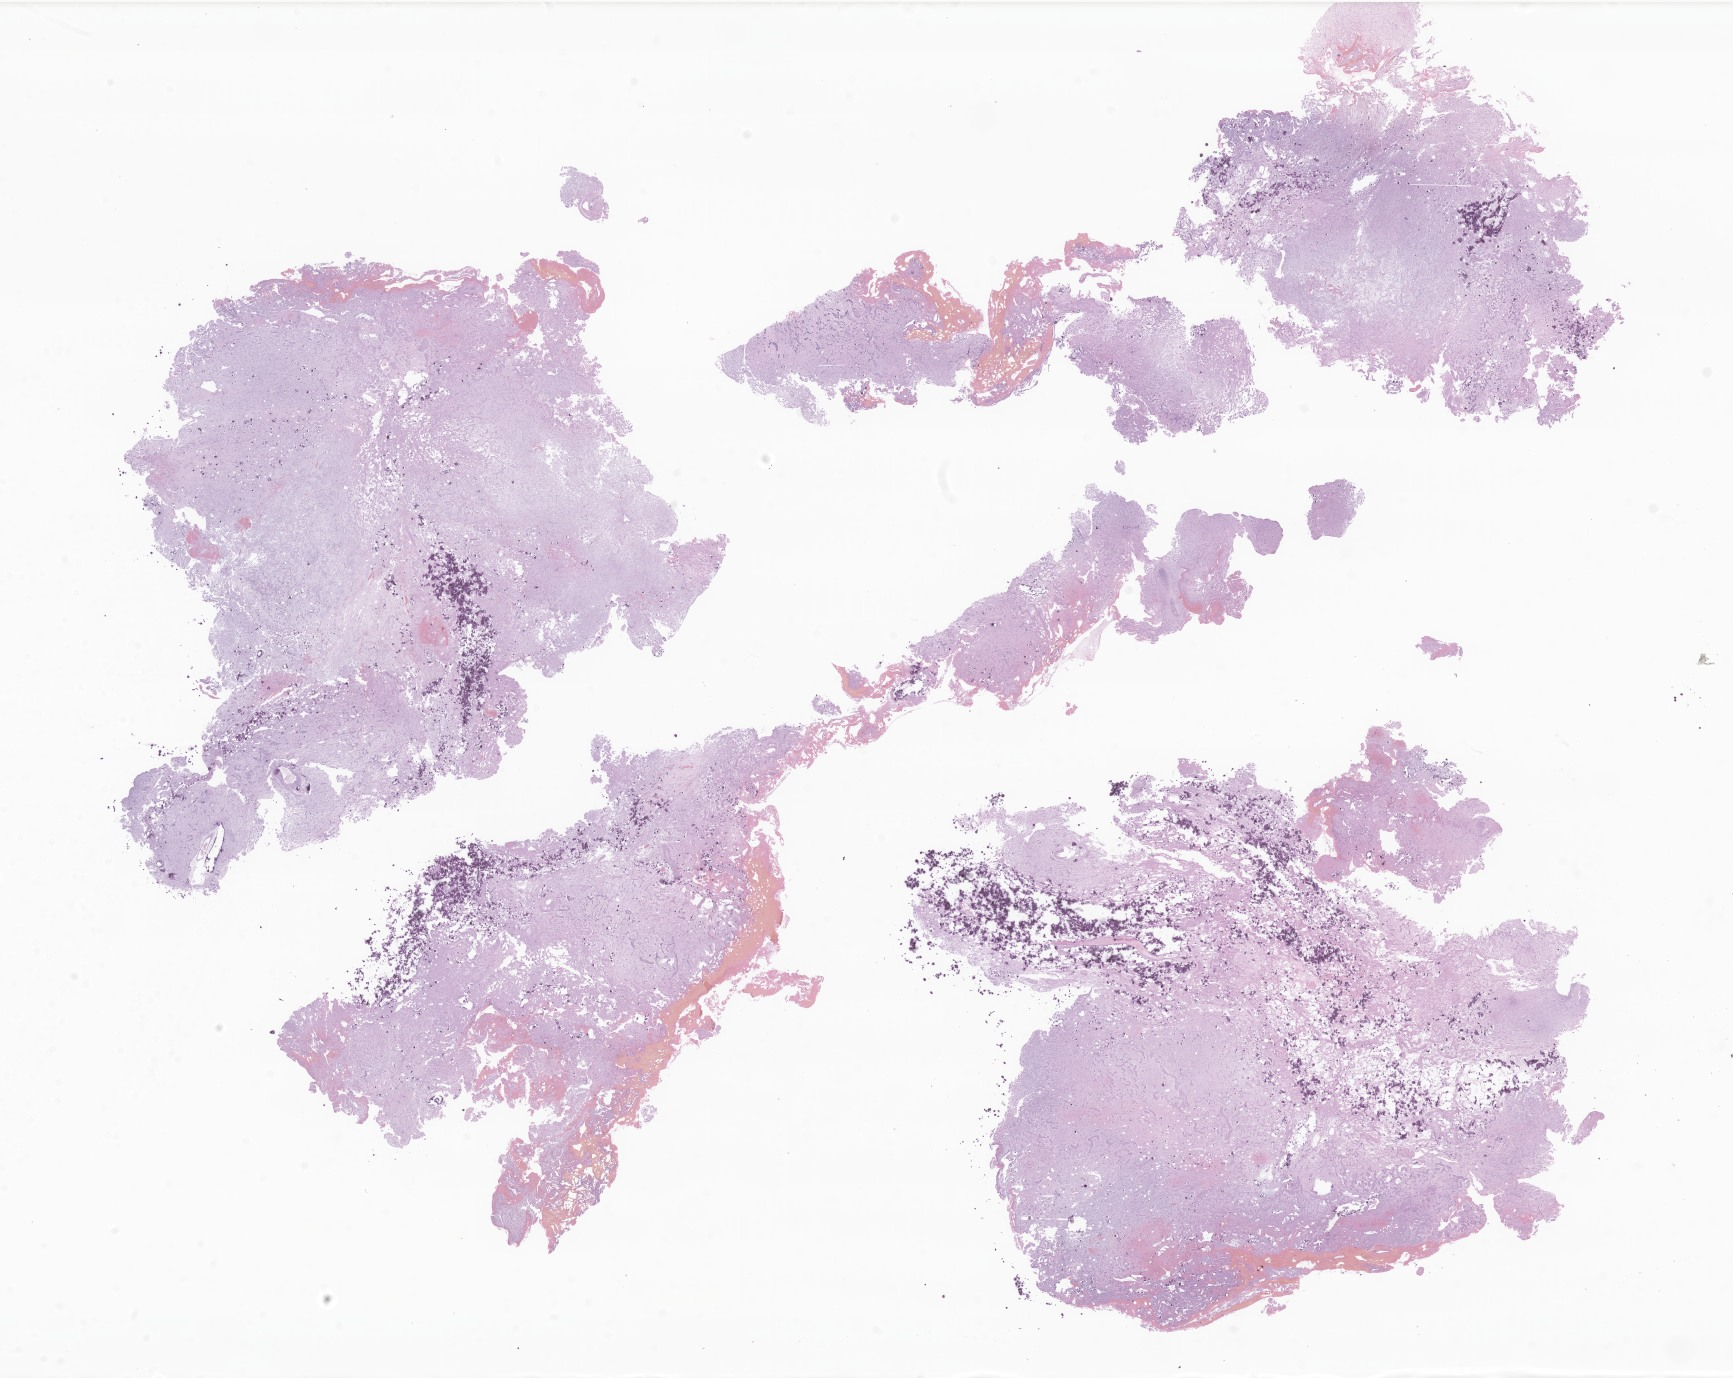
H&E whole-slide image of tumor tissue from the brain — low-resolution overview of the scanned area, about 29.2 x 23.2 mm, FFPE section. Patient male; age 215 months (17 years 11 months).
Recorded diagnosis: Glioma, malignant.